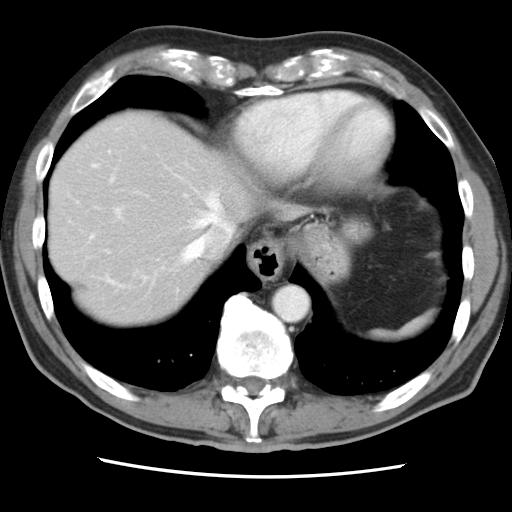
Contrast-enhanced abdominal CT, one axial slice. Position 72 of 83 along the scan axis. Intravenous contrast given. Soft-tissue window (W 400 / L 40 HU). 5 mm slice thickness. 512 × 512 image matrix, field of view 321 × 321 mm. Male patient, age 69 years. From the clinical record (not read from this slice): diagnosis: colorectal cancer liver metastases, imaged before liver resection; multiple liver metastases: yes; largest metastasis: 3.5 cm; disease in both lobes: no.
Outlined on this slice (expert manual segmentation):
- hepatic veins: bounding box (x1, y1, x2, y2) in pixels: (90, 164, 233, 287)
- liver: (50, 111, 258, 327)
- planned liver remnant (the part of the liver to remain after resection): (50, 151, 212, 327)
- portal vein (with intrahepatic branches): (110, 176, 187, 218)